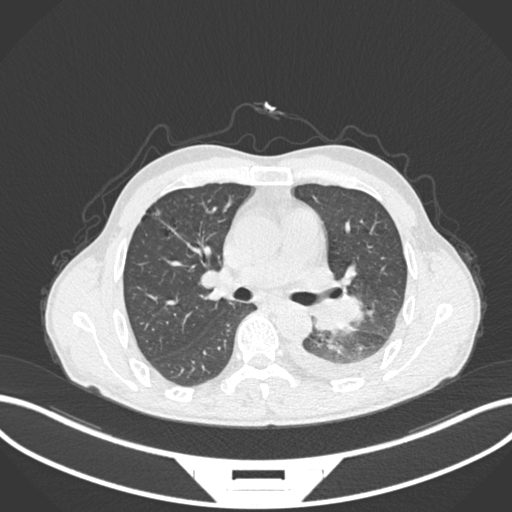
Chest CT, one axial slice. Slice 147 of 222 in the series (ordered by position). Reconstruction kernel B30f. 120 kVp. Lung window (W 1500 / L -600 HU). 512 × 512 image matrix, field of view 400 × 400 mm. Patient: male, 47 years. Case-level facts recorded for this patient, not image findings: clinical TNM (as recorded): T3 N1 M1c; histopathological grade: G3.
Structures marked on this image (bounding box drawn by a radiologist):
- lung tumour (recorded histology: small cell carcinoma): bounding box [x1, y1, x2, y2] px = [307, 293, 368, 336]